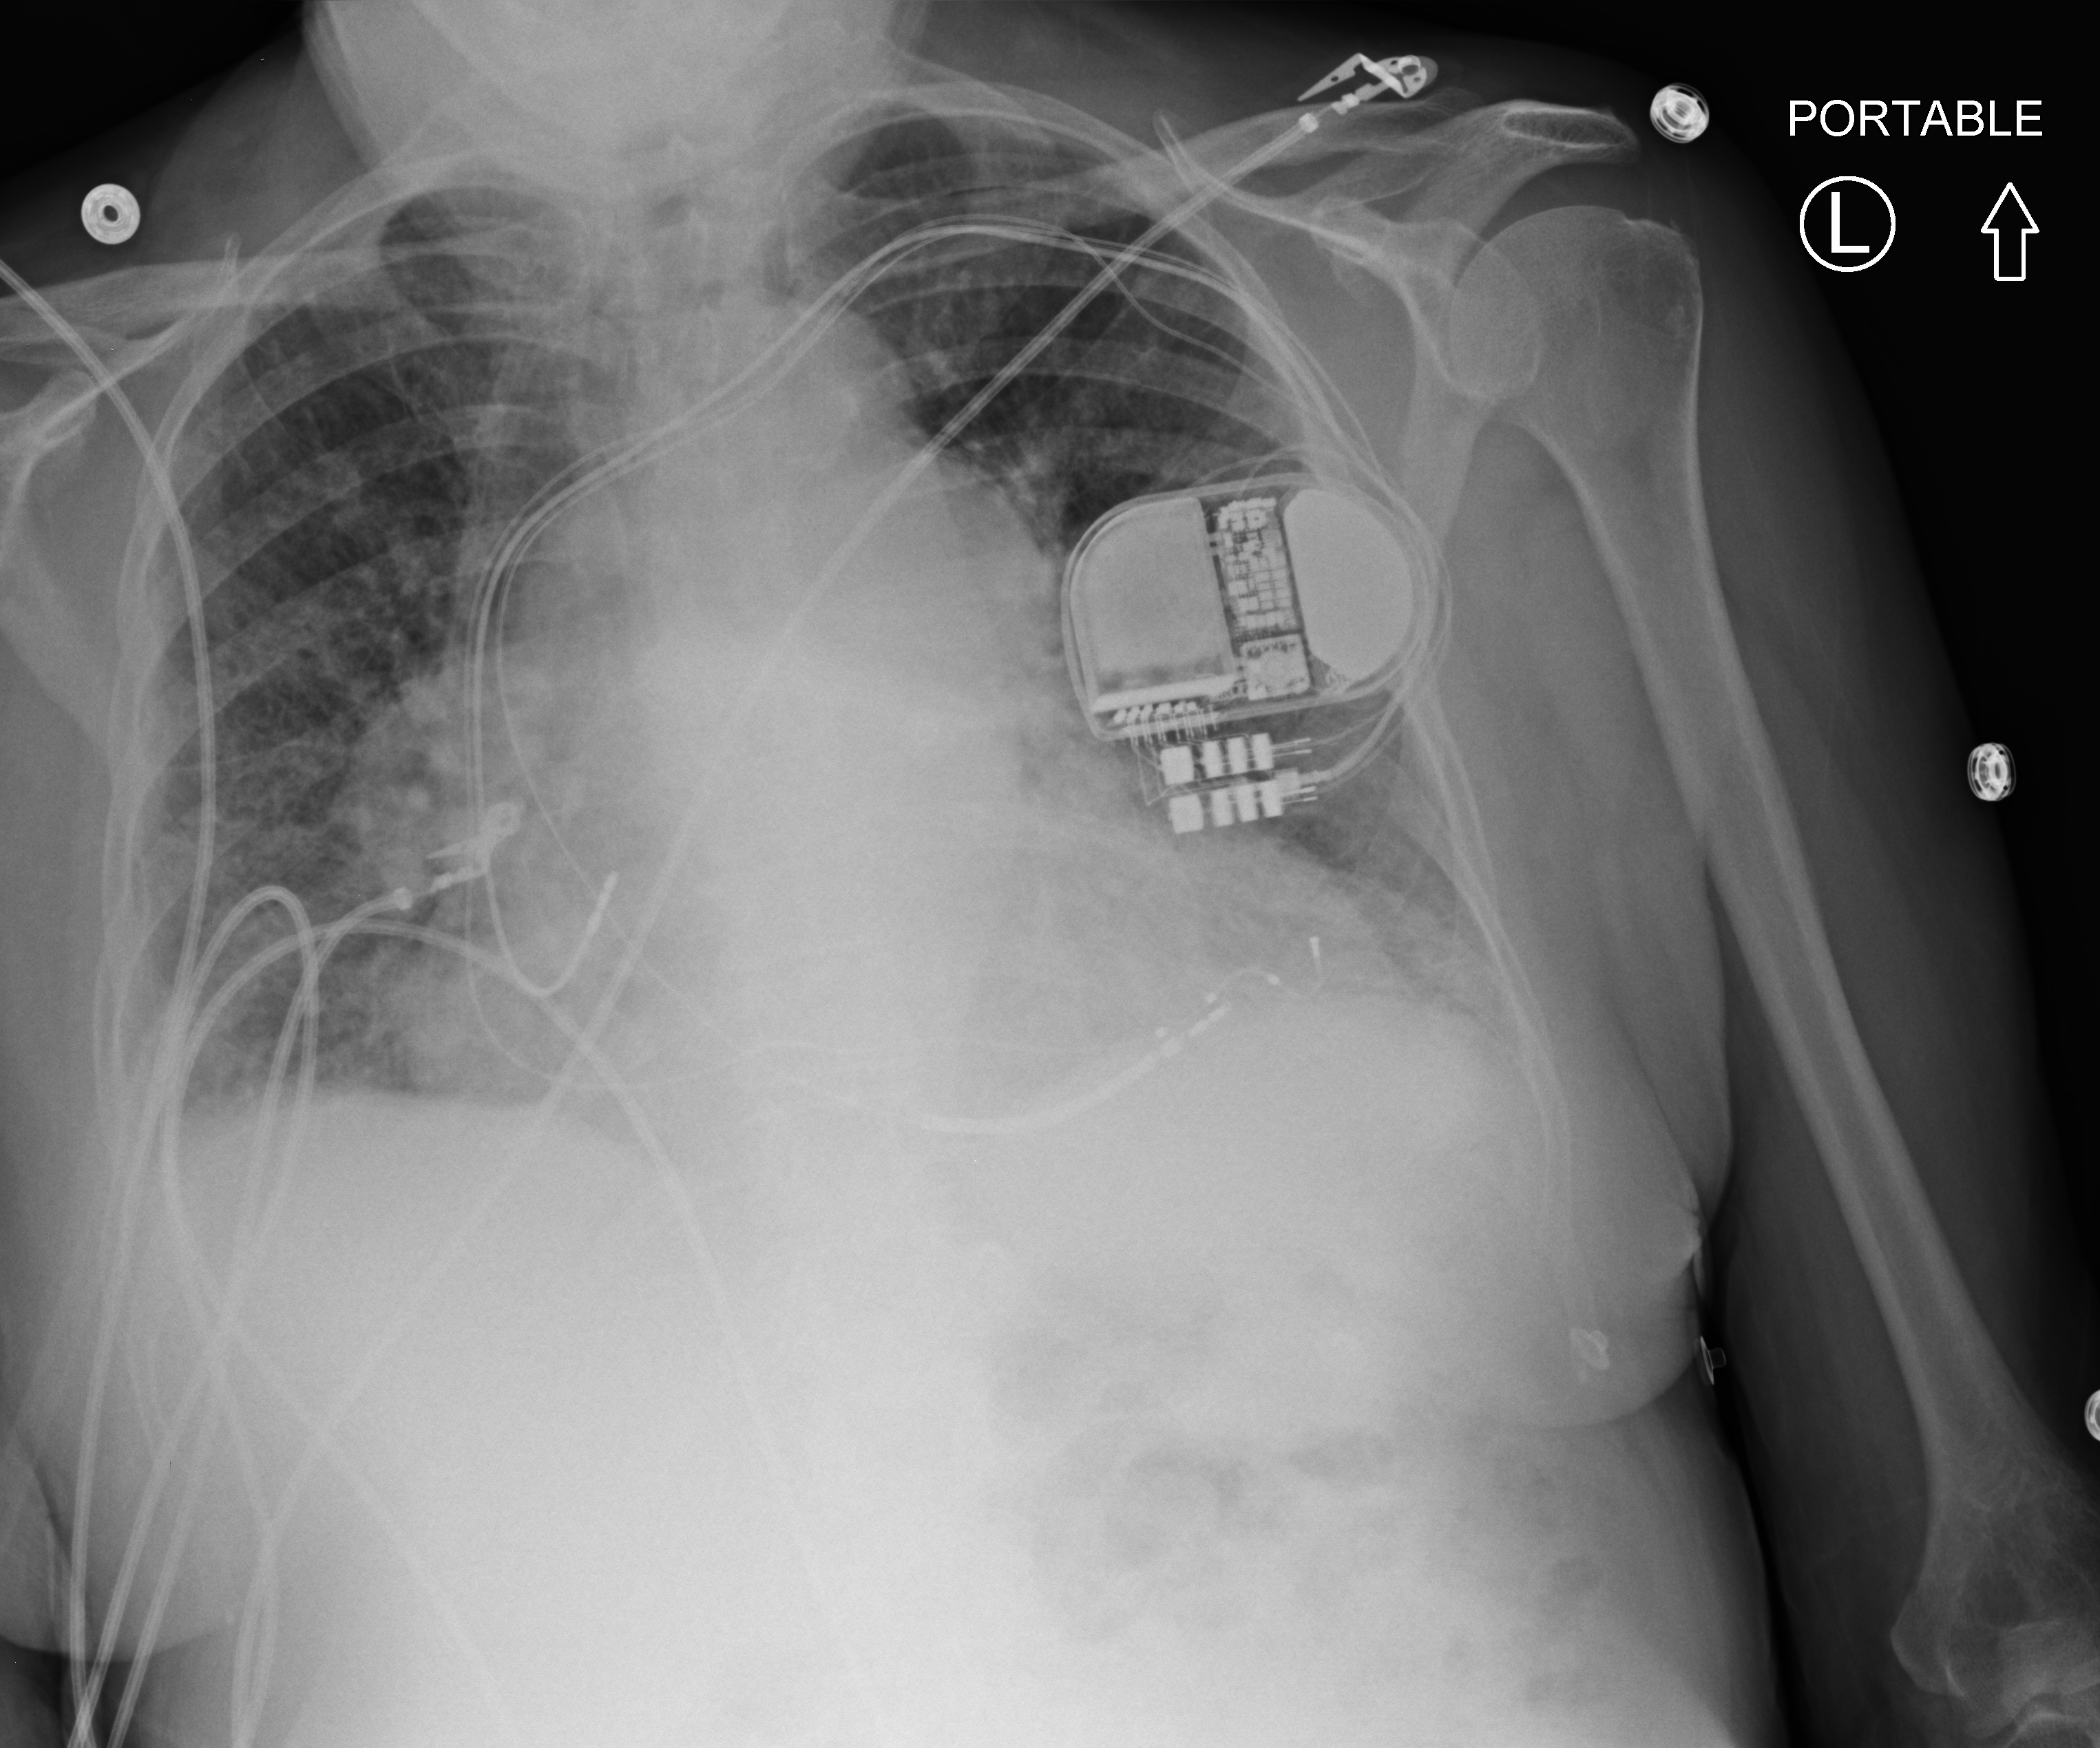
Portable chest radiograph. Patient hospitalised with COVID-19; female, aged 60–74 years.
Hospital-stay facts (about this admission, not read from this image; timing relative to this image not recorded): length of hospital stay: 6 days; mechanically ventilated during this hospital stay: no.